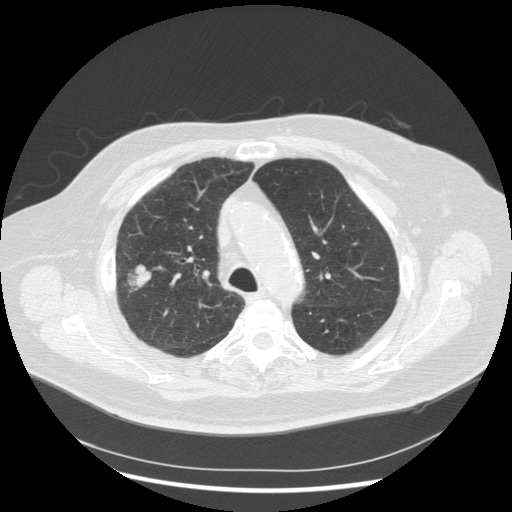
Low-dose screening chest CT, one axial slice. Slice 205 of 263 in the series (ordered by position). 120 kVp. Lung window (W 1500 / L -600 HU). 2.5 mm slice thickness. 512 × 512 image matrix.
Annotated regions visible in this slice (expert manual segmentation):
- lesion 1 (tumor, upper lobe of right lung): bounding box <134,265,151,287> (left, top, right, bottom; pixels)